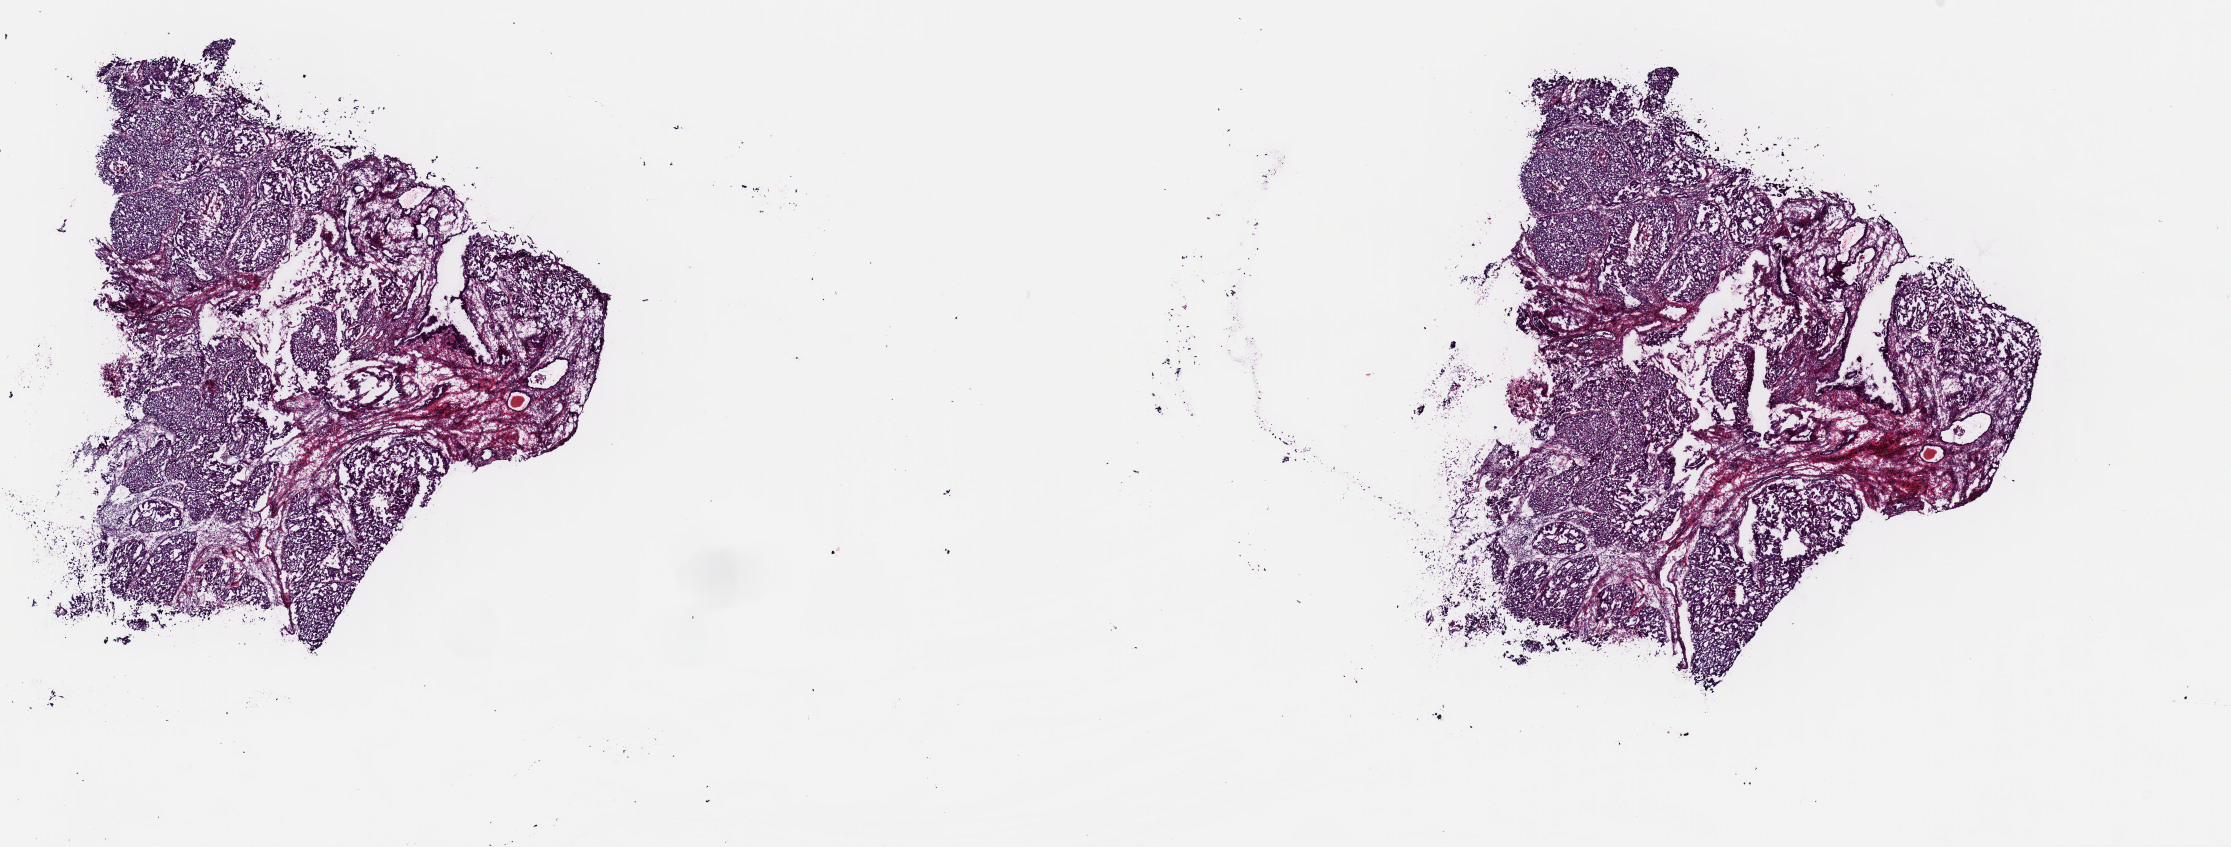
Whole-slide histology image, Hematoxylin and eosin (H&E) stained, whole scanned area (about 17.6 x 6.7 mm, from a 40x scan) shown as a low-resolution overview; frozen section from the top of the tissue portion; sample: primary tumour, uterus. Female patient; age at initial diagnosis 64 years. Histologic grade: G3 (poorly differentiated). Pathologist review of this section (percent, as recorded): tumour cells 70%, tumour nuclei 70%, normal cells 0%, stromal cells 20%, necrosis 10%. Inflammatory infiltration, as recorded: lymphocyte infiltration 40%, monocyte infiltration 20%, neutrophil infiltration 20%.
FIGO stage: II. Pathologic diagnosis: Serous cystadenocarcinoma, NOS (endometrium). Lymph nodes positive (case pathology): 0 of 6 examined.